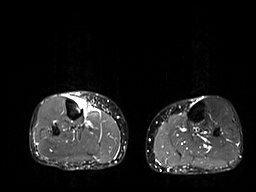
MRI of an extremity soft-tissue mass, one axial slice. Position 12 of 32 along the scan axis. STIR. 6 mm slice thickness. 256 × 192 image matrix. Female patient. Case-level facts recorded for this patient, not image findings: histological type: undifferentiated – high grade; grade: high; site of the primary tumour: right thigh.
Outlined on this slice (outlined manually by an expert reader):
- gross tumour volume (mass): bounding box [x1, y1, x2, y2] px = [71, 96, 89, 114]